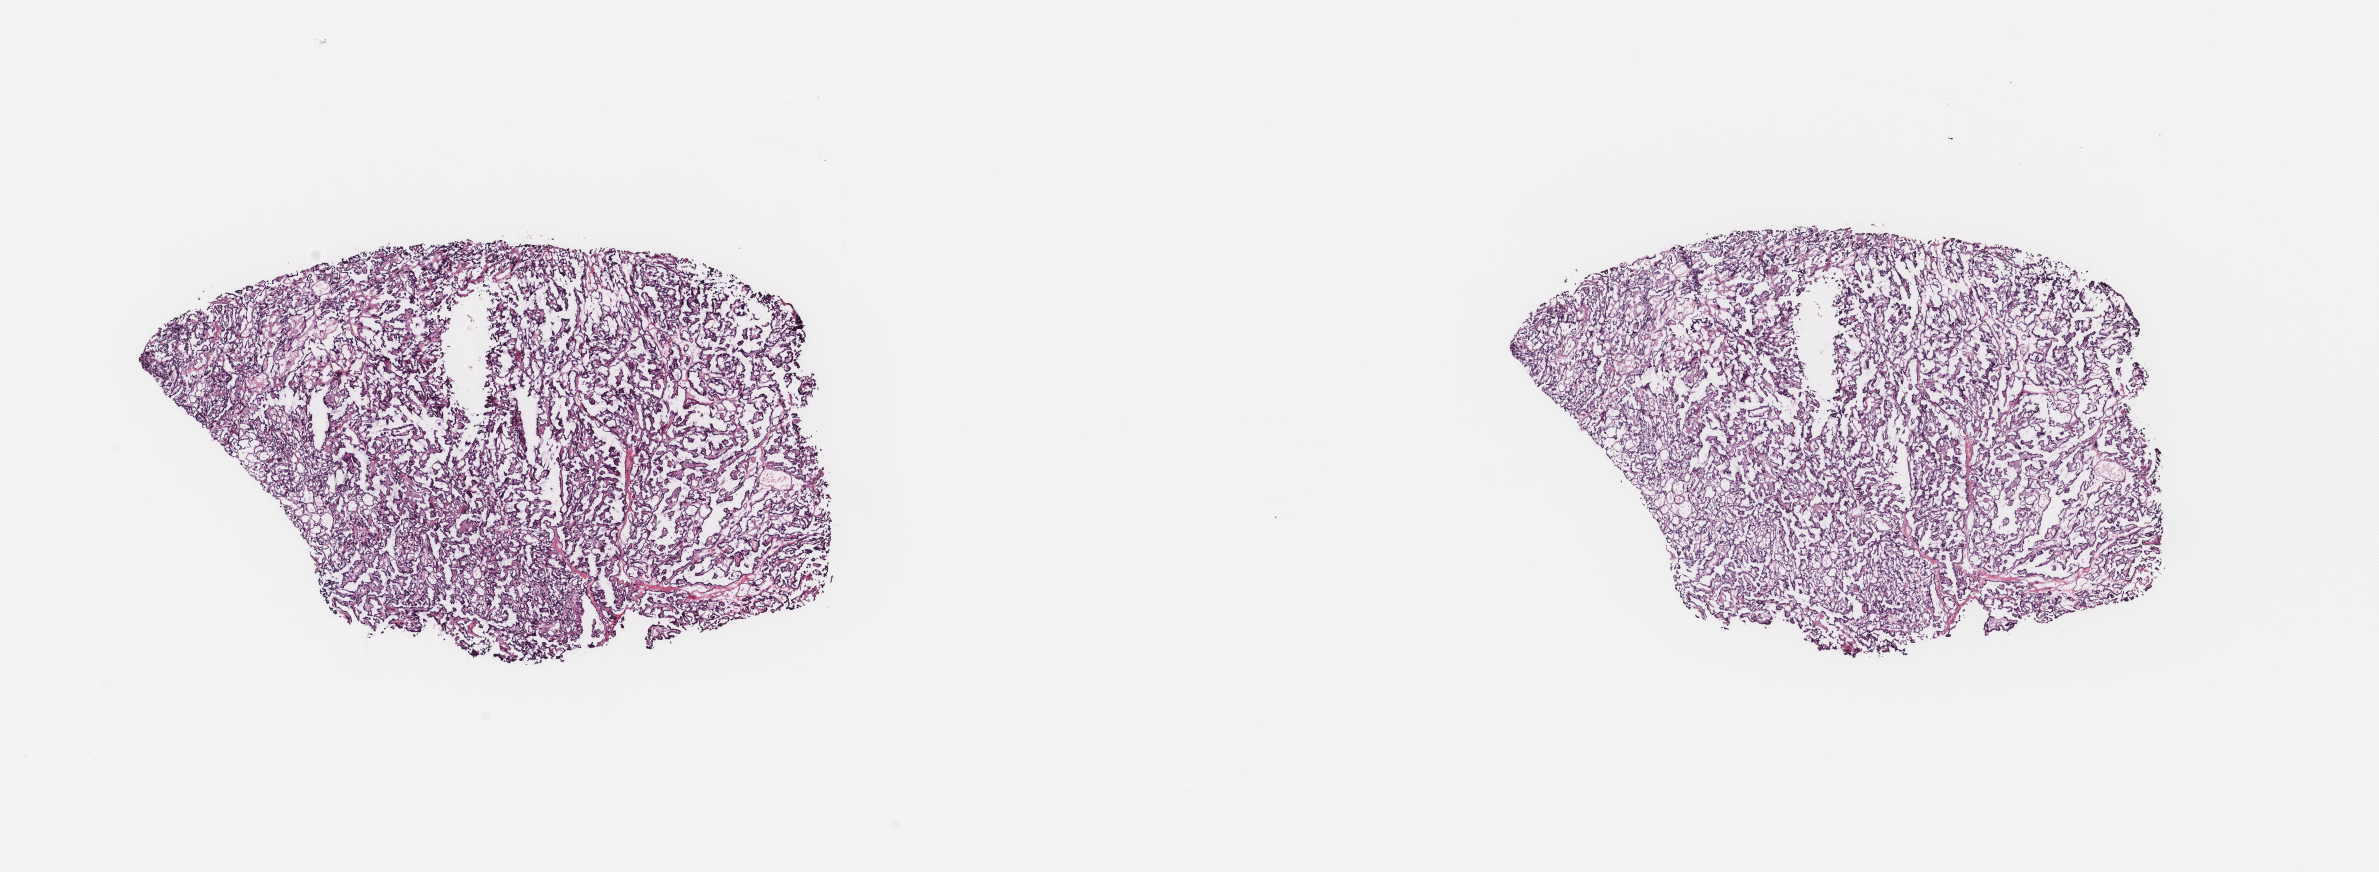
Whole-slide histology image, Hematoxylin and eosin (H&E) stained — whole scanned area (about 18.9 x 6.9 mm, acquisition: 40x scan) shown as a low-resolution overview. Frozen section from the top of the tissue portion. Sample: primary tumour, thyroid. Female patient; age at initial diagnosis 85 years. Slide review estimates, as recorded: tumour cells 70%, tumour nuclei 100%, normal cells 0%, stromal cells 30%, necrosis 0%. Inflammatory infiltration, as recorded: lymphocyte infiltration 0%, monocyte infiltration 1%, neutrophil infiltration 0%.
- laterality: left
- AJCC pathologic stage: I
- TNM: T1b N0 MX
- histologic diagnosis: Papillary adenocarcinoma, NOS